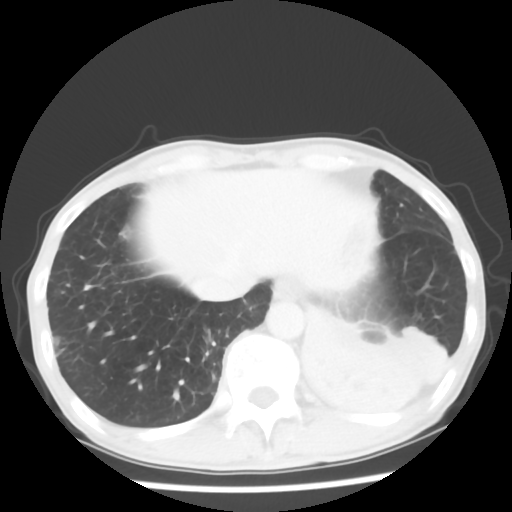
Chest CT, one axial slice; position 11 of 64 along the scan axis; lung window (W 1500 / L -600 HU); 5 mm slice thickness; 512 × 512 image matrix, field of view 313 × 313 mm. Patient: male, 68 years. Case-level facts recorded for this patient, not image findings: clinical TNM (as recorded): T4 N0 M0.
Outlined on this slice (bounding box drawn by a radiologist):
- lung tumour (recorded histology: squamous cell carcinoma): bounding box (x1, y1, x2, y2) in pixels: (291, 310, 468, 421)